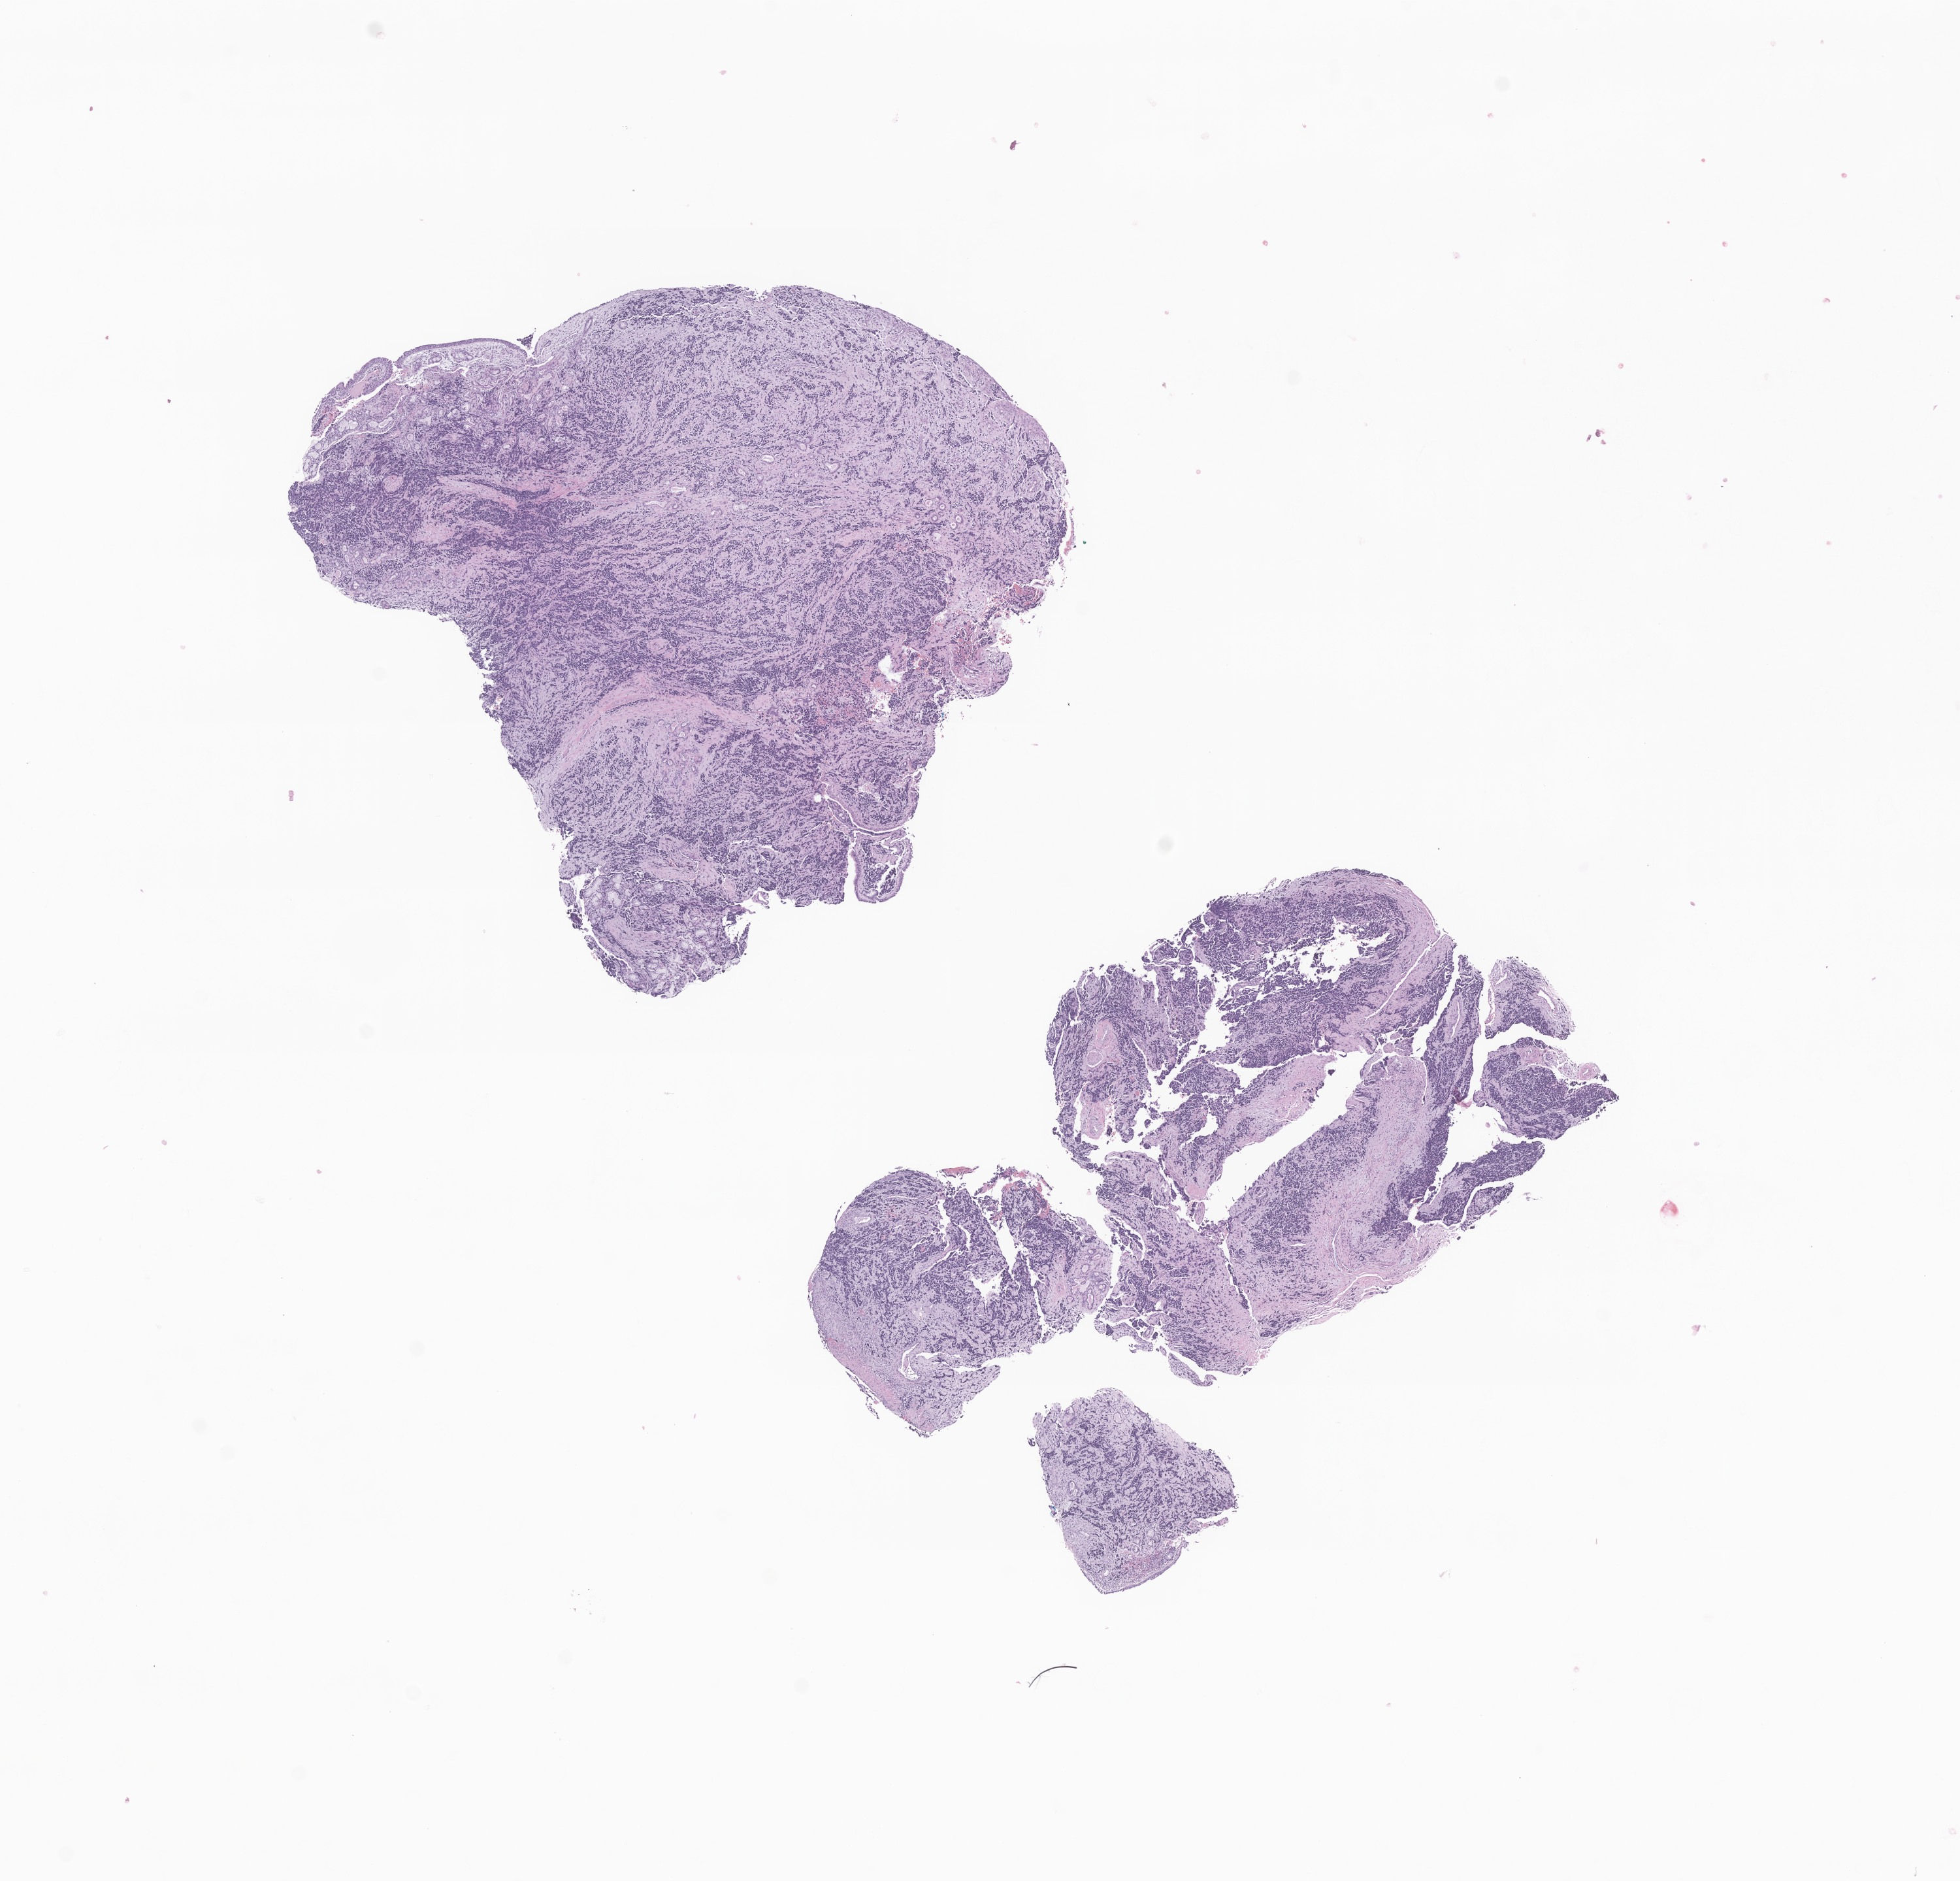
Whole-slide image, haematoxylin and eosin stain of tumor tissue from the soft tissue — whole scanned area (about 12.6 x 12.1 mm) shown as a low-resolution overview, formalin-fixed paraffin-embedded section. Patient female; age 200 months (16 years 8 months).
Recorded diagnosis: Alveolar rhabdomyosarcoma.